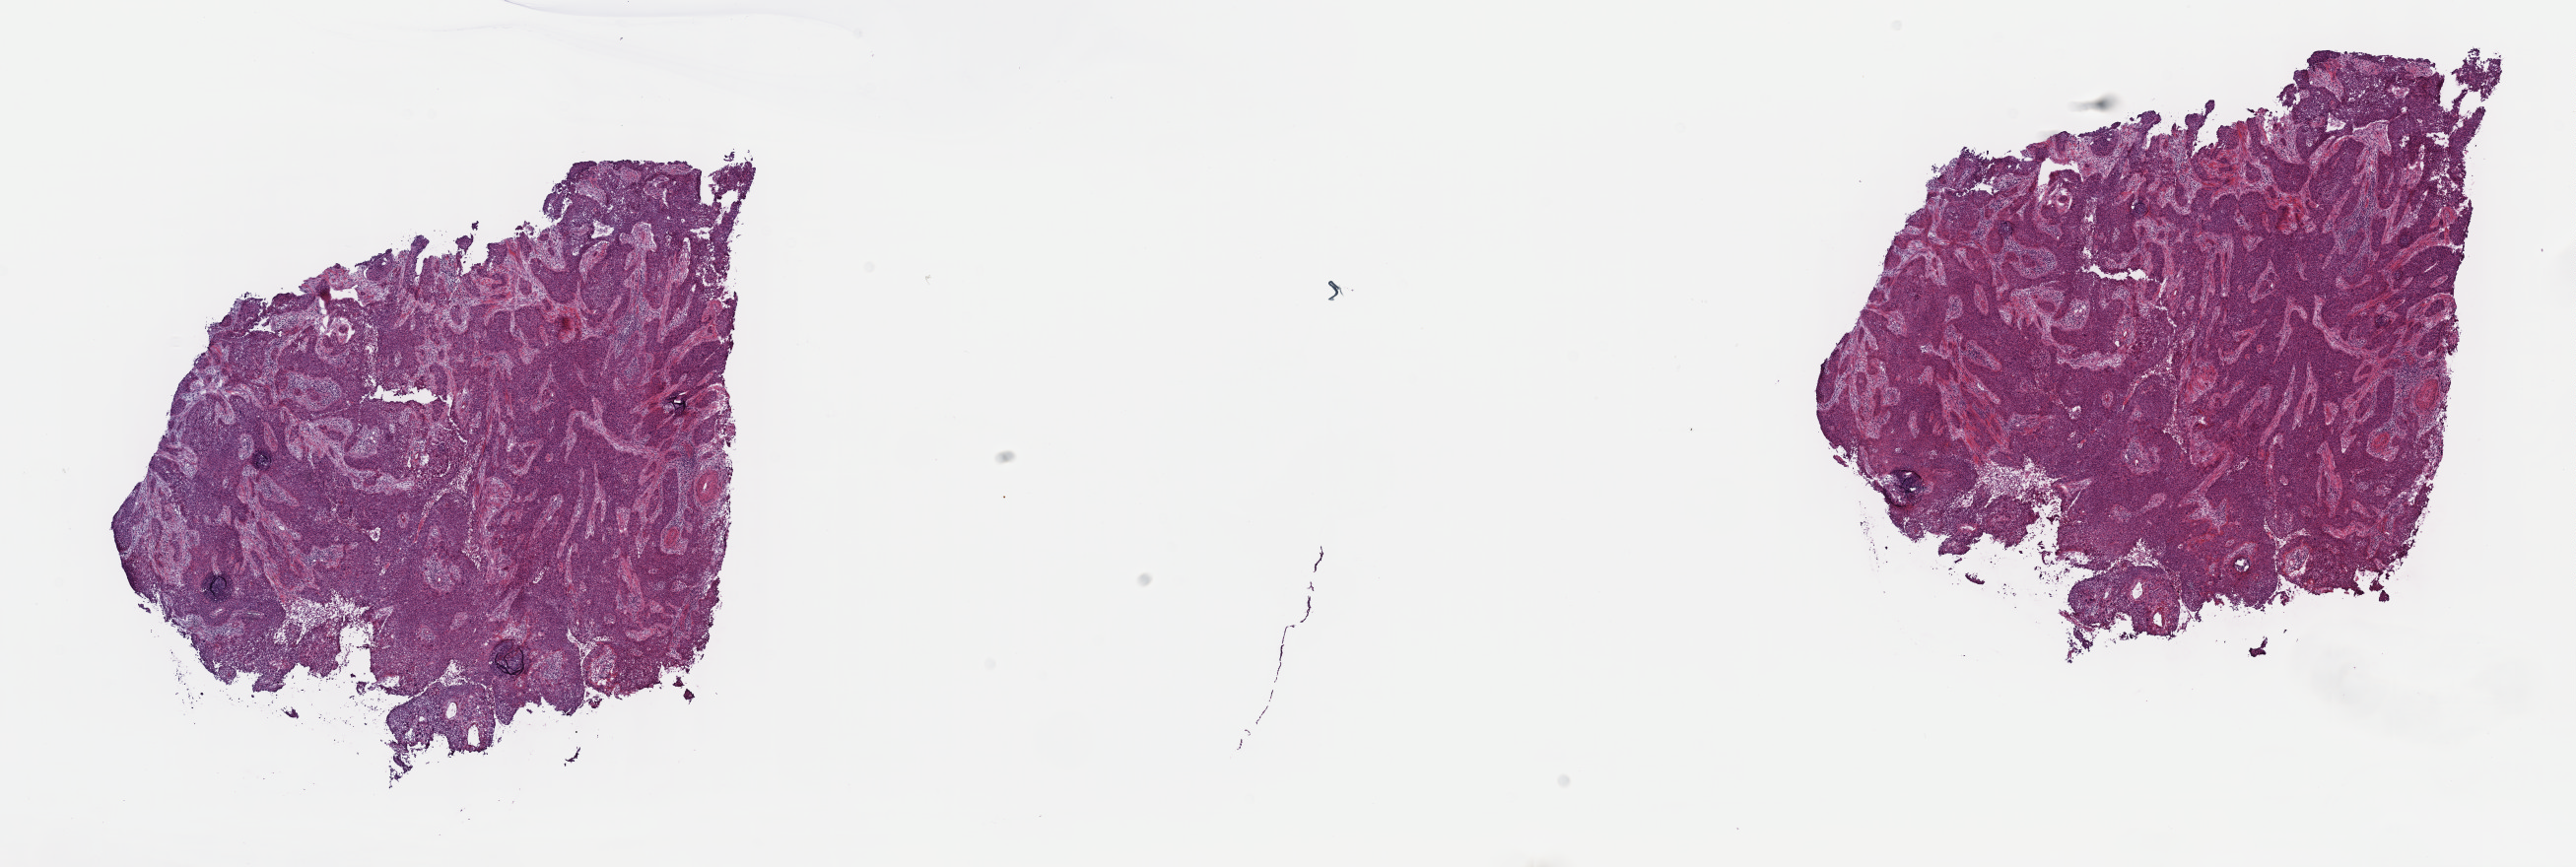
Whole-slide histology image, H&E, a low-resolution overview of the entire scanned area, about 21.1 x 7.1 mm, frozen section from the top of the tissue portion, primary tumour sample from the cervix. Patient: female, age at initial diagnosis 27 years. Histologic grade: G3 (poorly differentiated). Slide review estimates, as recorded: tumour cells 70%, tumour nuclei 70%, normal cells 15%, stromal cells 13%, necrosis 2%. Infiltration values recorded for this section: lymphocyte infiltration 10%, monocyte infiltration 0%, neutrophil infiltration 2%.
• lymph nodes positive (case pathology): 0 of 15 examined
• diagnosis: Squamous cell carcinoma, NOS
• FIGO stage: IB1